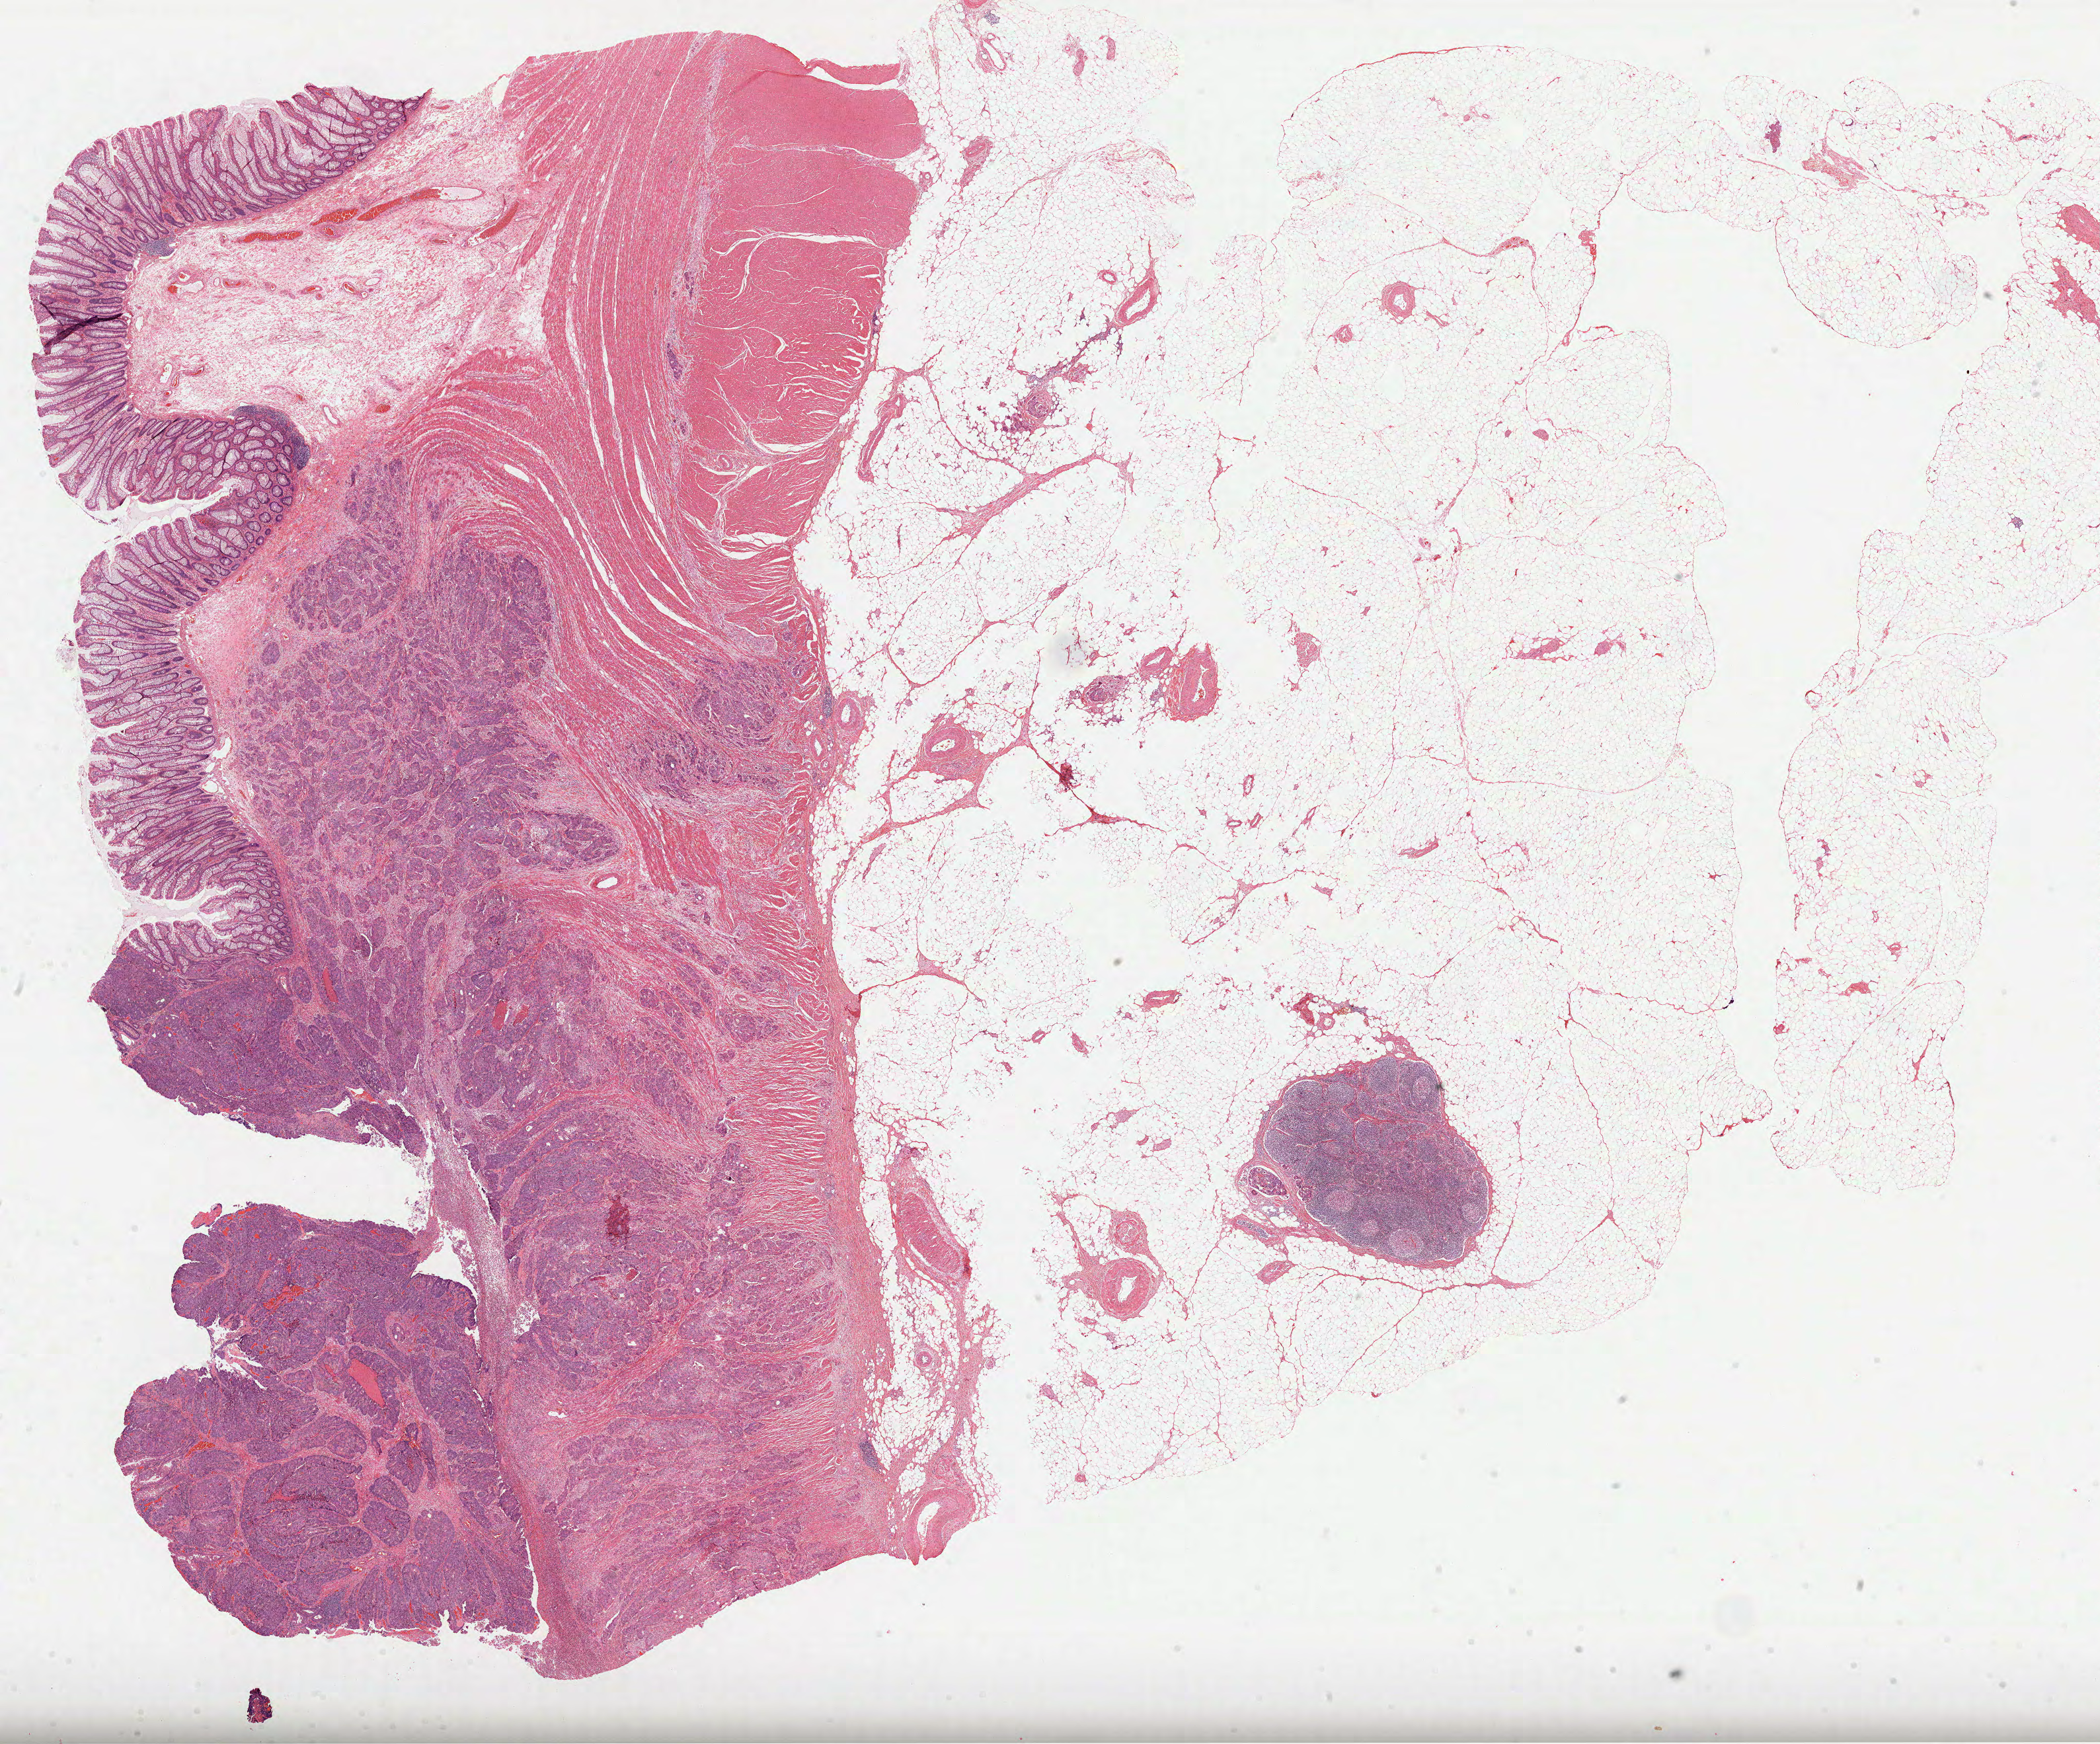
Digitized H&E-stained tissue section (whole slide), shown as a low-resolution overview of the whole scanned area (about 25.6 x 21.3 mm), FFPE section, rectum, primary tumour sample. Female, age 71 years at initial diagnosis.
• AJCC pathologic stage: IIIC
• diagnosis: Adenocarcinoma, NOS
• TNM: T3 N2 MX